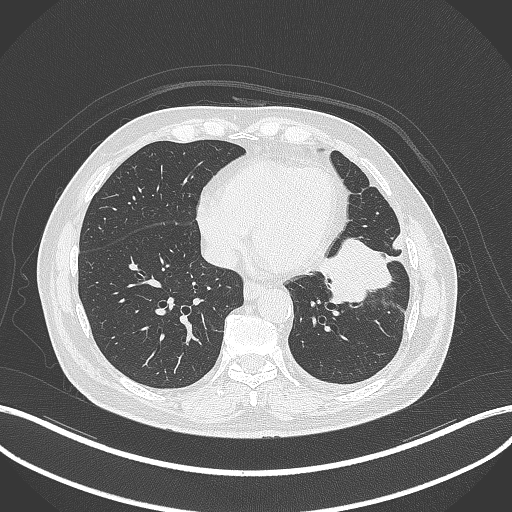
Chest CT, one axial slice; slice 120 of 230 in the series (ordered by position); 120 kVp; lung window (W 1500 / L -600 HU); 512 × 512 image matrix, field of view 400 × 400 mm. Patient: male, 68 years. From the clinical record (not read from this slice): clinical TNM (as recorded): T2b N0 M0.
Outlined on this slice (rectangle marked by the reading radiologist):
- lung tumour (recorded histology: squamous cell carcinoma): bounding box <315,228,397,308> (left, top, right, bottom; pixels)